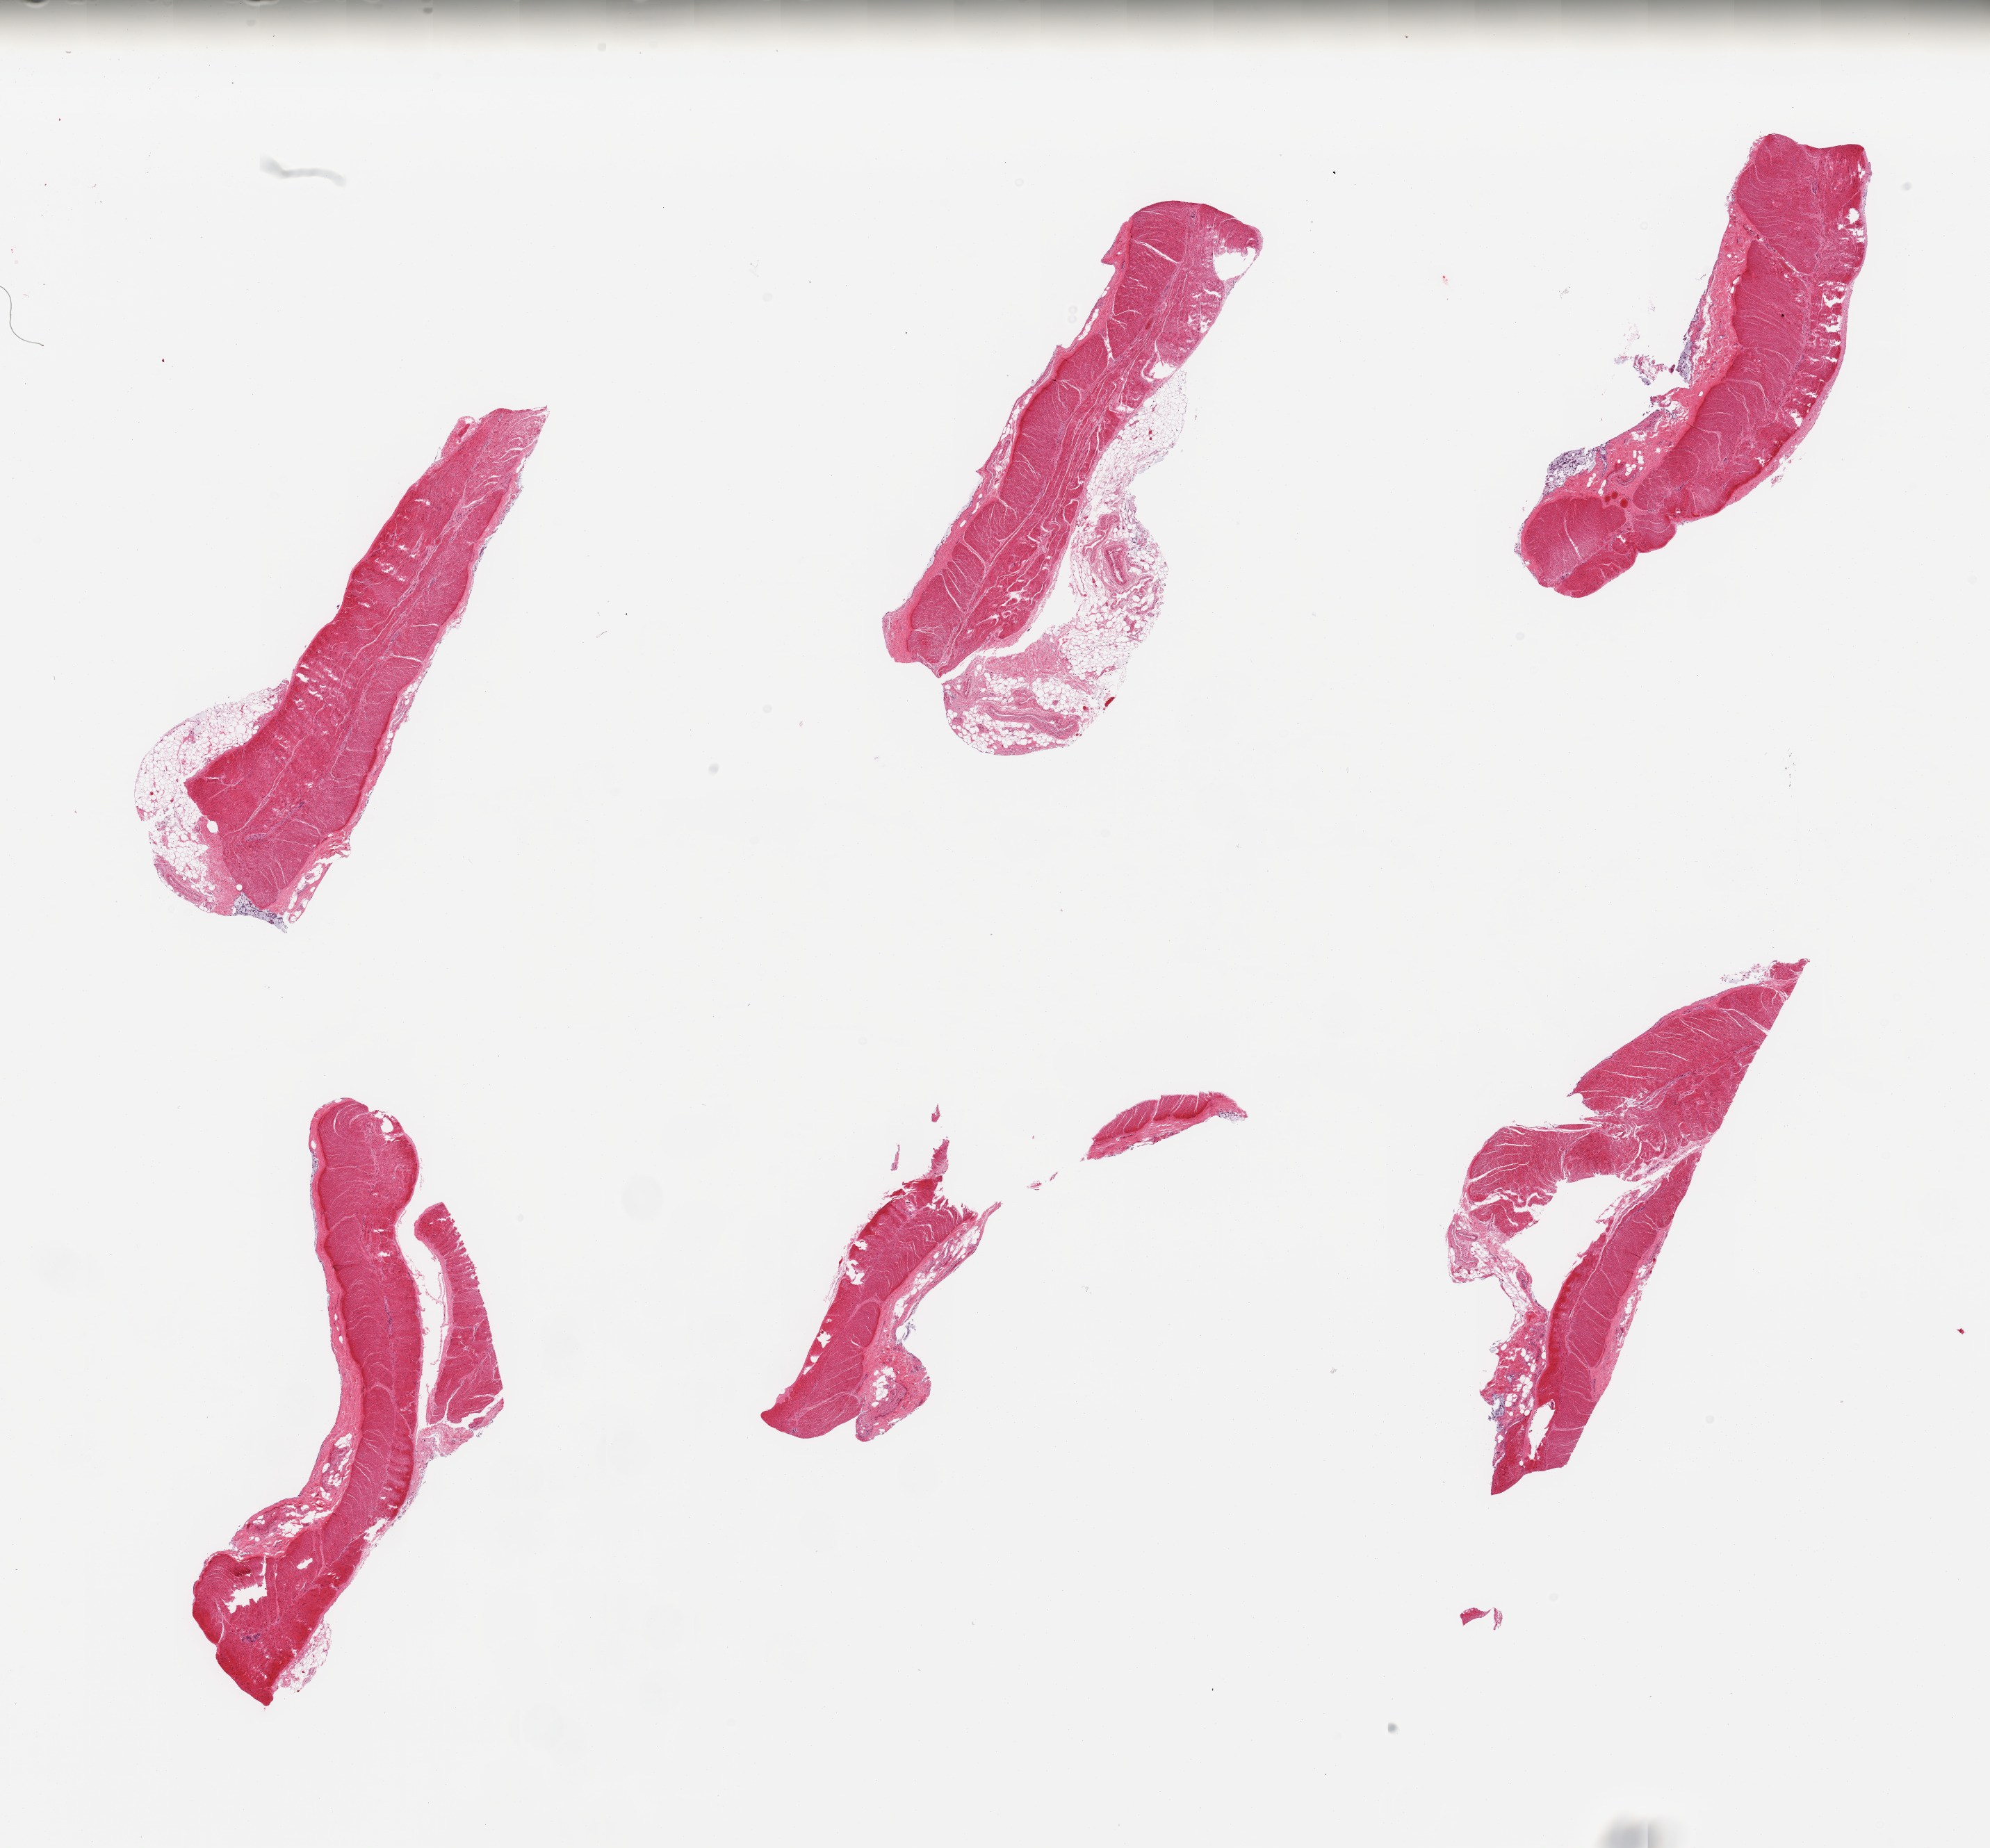
Whole-slide image, H&E stain — shown as a low-resolution overview of the whole scanned area (about 22.6 x 21.0 mm). PAXgene-fixed paraffin-embedded (PFPE) section. Sampled site (target tissue): sigmoid colon. Tissue donor sample. Donor: male.
- review note (as recorded): 6 pieces; fat, fibrous stroma and mucus adherent to several pieces